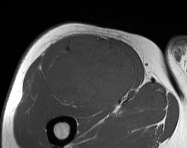
MRI of an extremity soft-tissue mass, one axial slice. Position 93 of 114 along the scan axis. MR volume resampled by the dataset authors to the PET/CT grid (not the native acquisition matrix). 3.27 mm slice thickness. 187 × 148 image matrix, field of view 183 × 145 mm. Male patient. Case-level facts recorded for this patient, not image findings: histological type: pleiomorphic leiomyosarcoma; grade: intermediate; site of the primary tumour: right thigh.
Outlined on this slice (expert contour drawn on MRI and transferred to this co-registered scan by the dataset authors):
- gross tumour volume including surrounding oedema: bounding box (x1, y1, x2, y2) in pixels: (45, 34, 137, 110)
- gross tumour volume (mass): (47, 34, 137, 110)